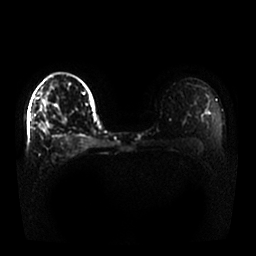
Breast MRI, one axial slice. Position 16 of 25 along the scan axis. Diffusion-weighted series; image 2 of 4 stored at this slice position (different b-values; order by instance number). 1.5 T. 4 mm slice thickness. 256 × 256 image matrix, field of view 370 × 370 mm. Female patient.
Annotated regions visible in this slice (expert manual segmentation):
- tumour on diffusion-weighted imaging: bounding box (x1, y1, x2, y2) in pixels: (39, 125, 47, 134)